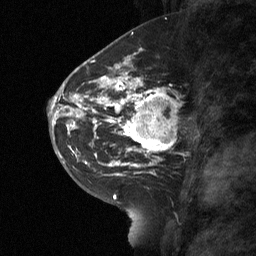
Breast MRI (dynamic contrast-enhanced), one sagittal slice; slice 29 of 64 in the series (ordered by position); dynamic contrast-enhanced study with each time point stored as its own series, time point 2 of 3 at this slice position (early post-contrast, ordered by acquisition time); 1.5 T; TE 4.8 ms, TR 27 ms; 256 × 256 image matrix. Patient: female, 42 years. Case-level facts recorded for this patient, not image findings: setting: breast cancer imaged before/during neoadjuvant chemotherapy; receptor status: triple-negative.
Outlined on this slice (semi-automatic segmentation, software-assisted and operator-edited):
- analysis volume of interest (the breast-tissue region the enhancement analysis was run in; not a lesion): bounding box (x1, y1, x2, y2) in pixels: (115, 85, 176, 160)
- tumour enhancement mask (voxels above the 90 % enhancement threshold inside the analysis volume of interest): (115, 85, 170, 159)